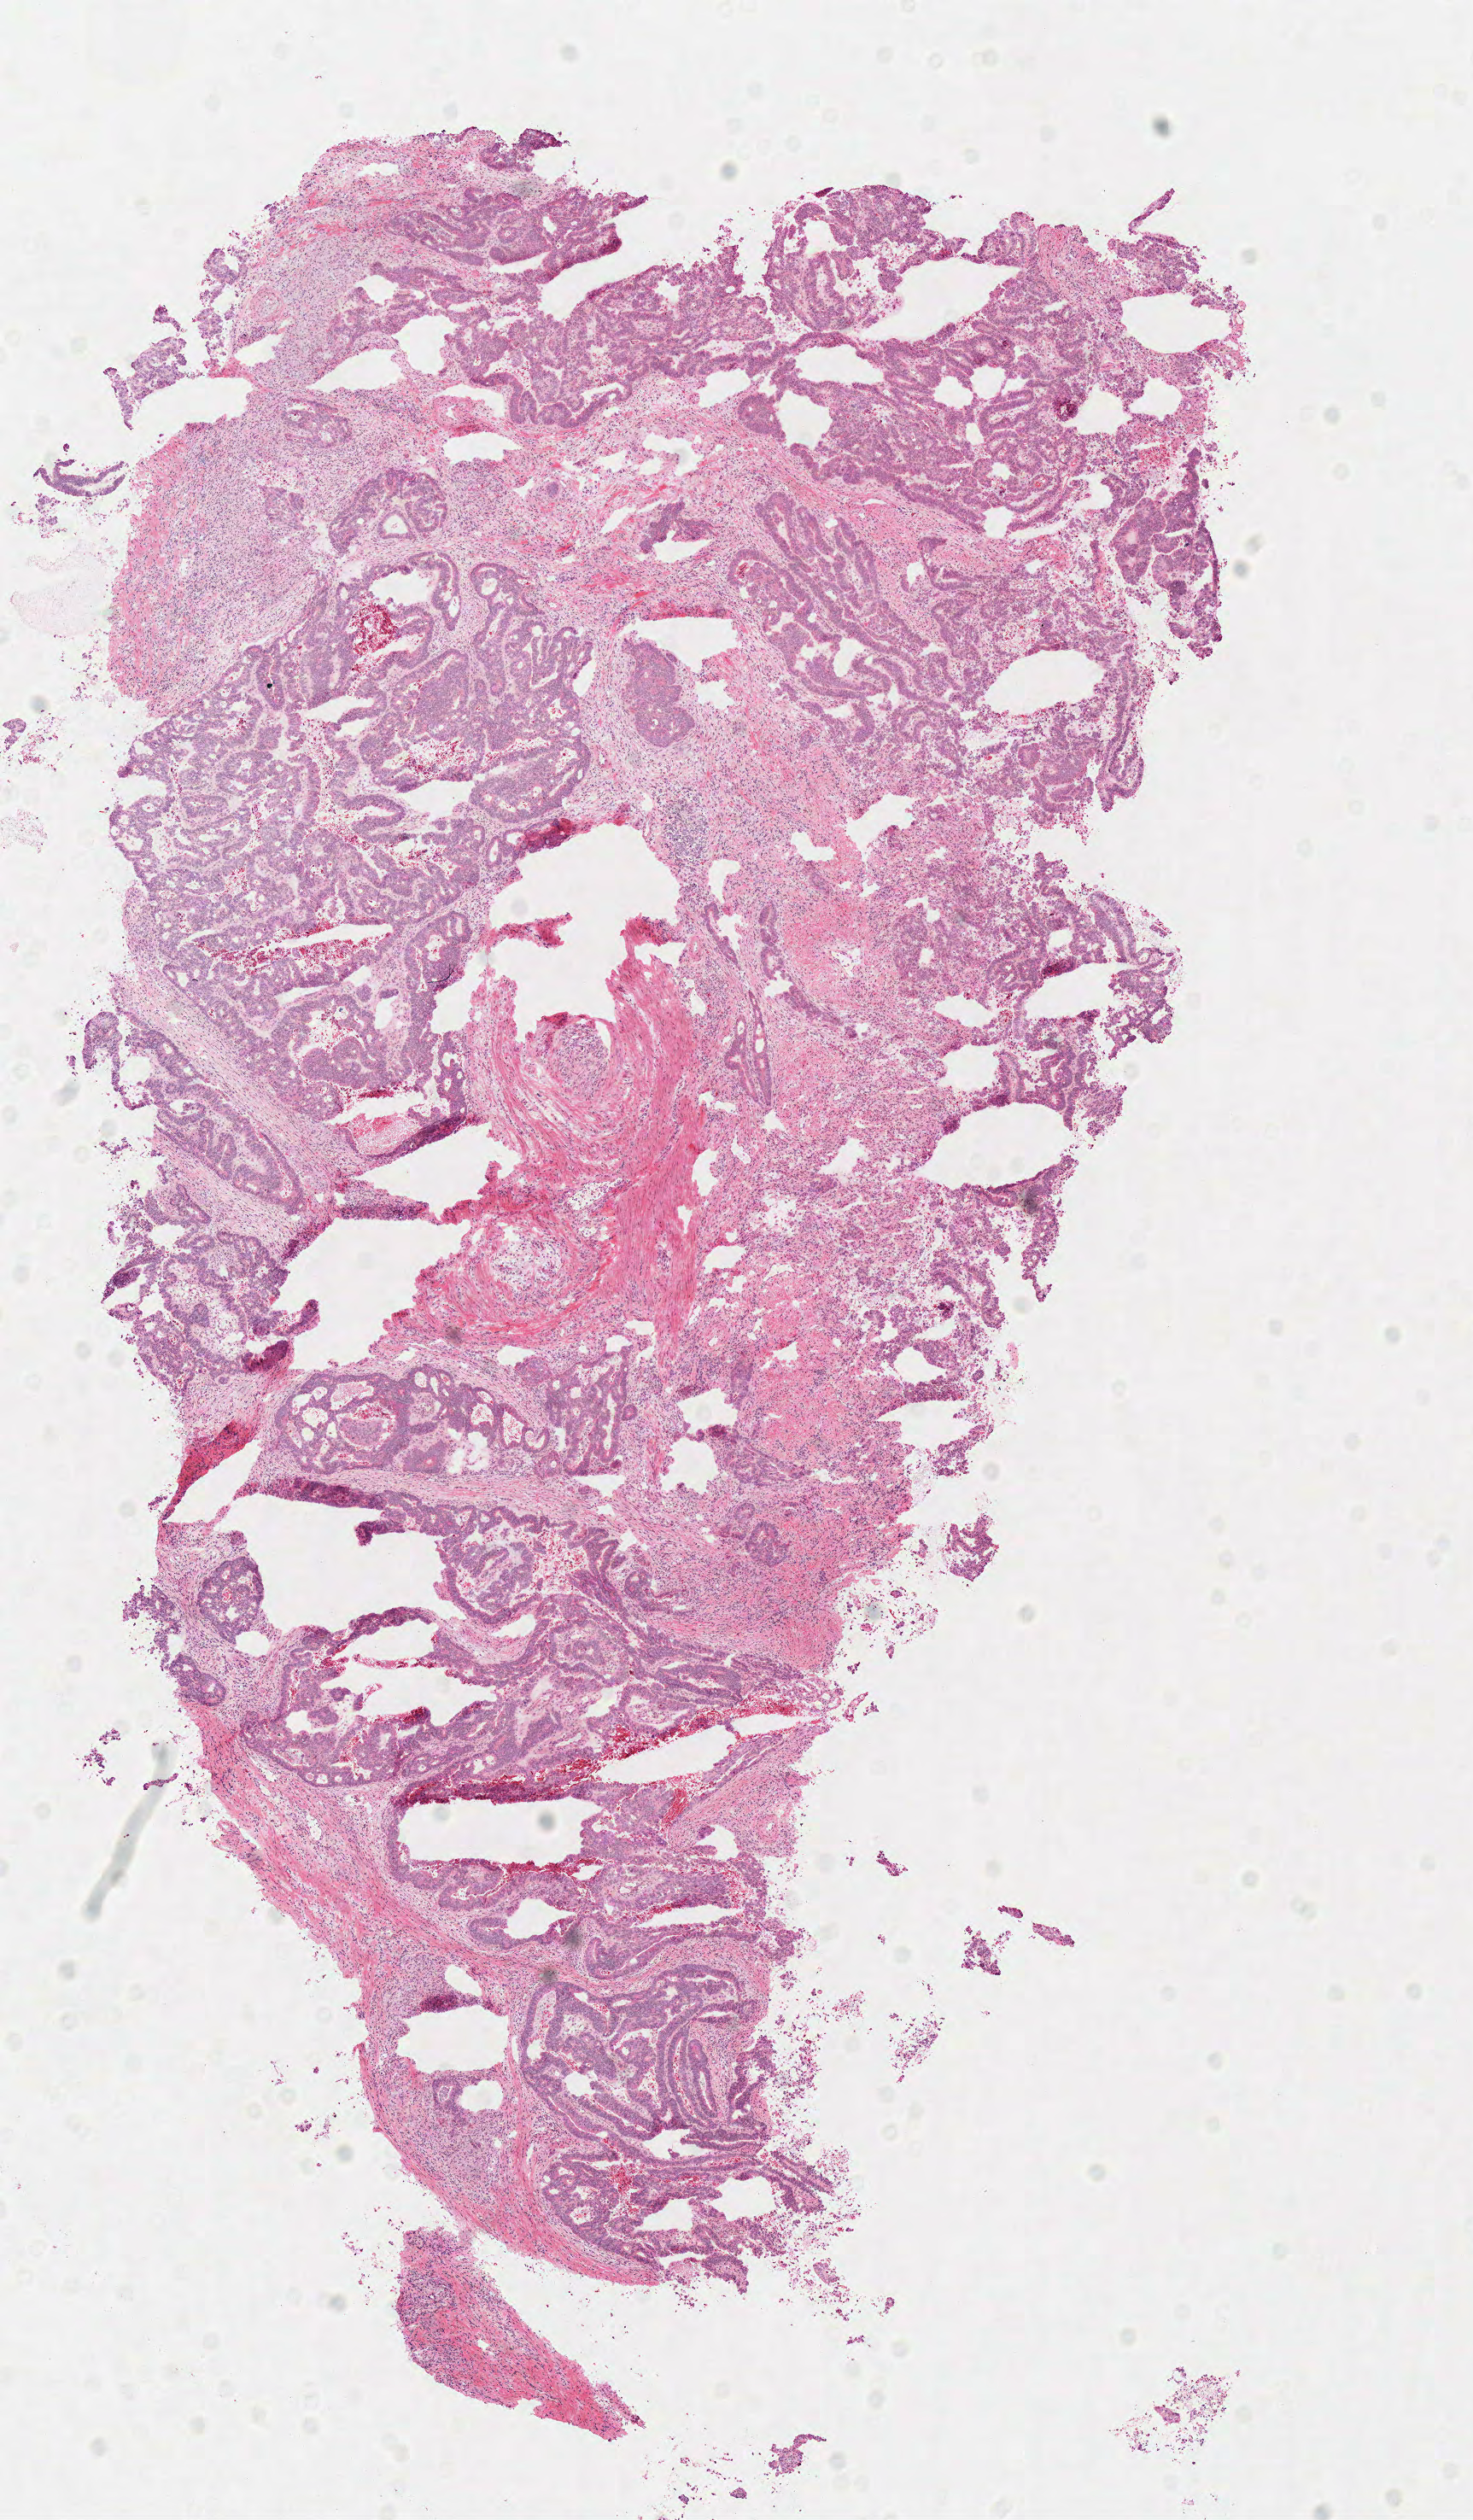
Digitized H&E-stained tissue section (whole slide), low-resolution overview of the scanned area, about 6.8 x 11.6 mm (acquisition: 40x scan), frozen section, primary tumour sample from the colon. Male, age 67 years at initial diagnosis. Composition of this section per pathologist review: tumour cells 68%, tumour nuclei 75%.
Pathologic diagnosis: Adenocarcinoma, NOS (cecum).